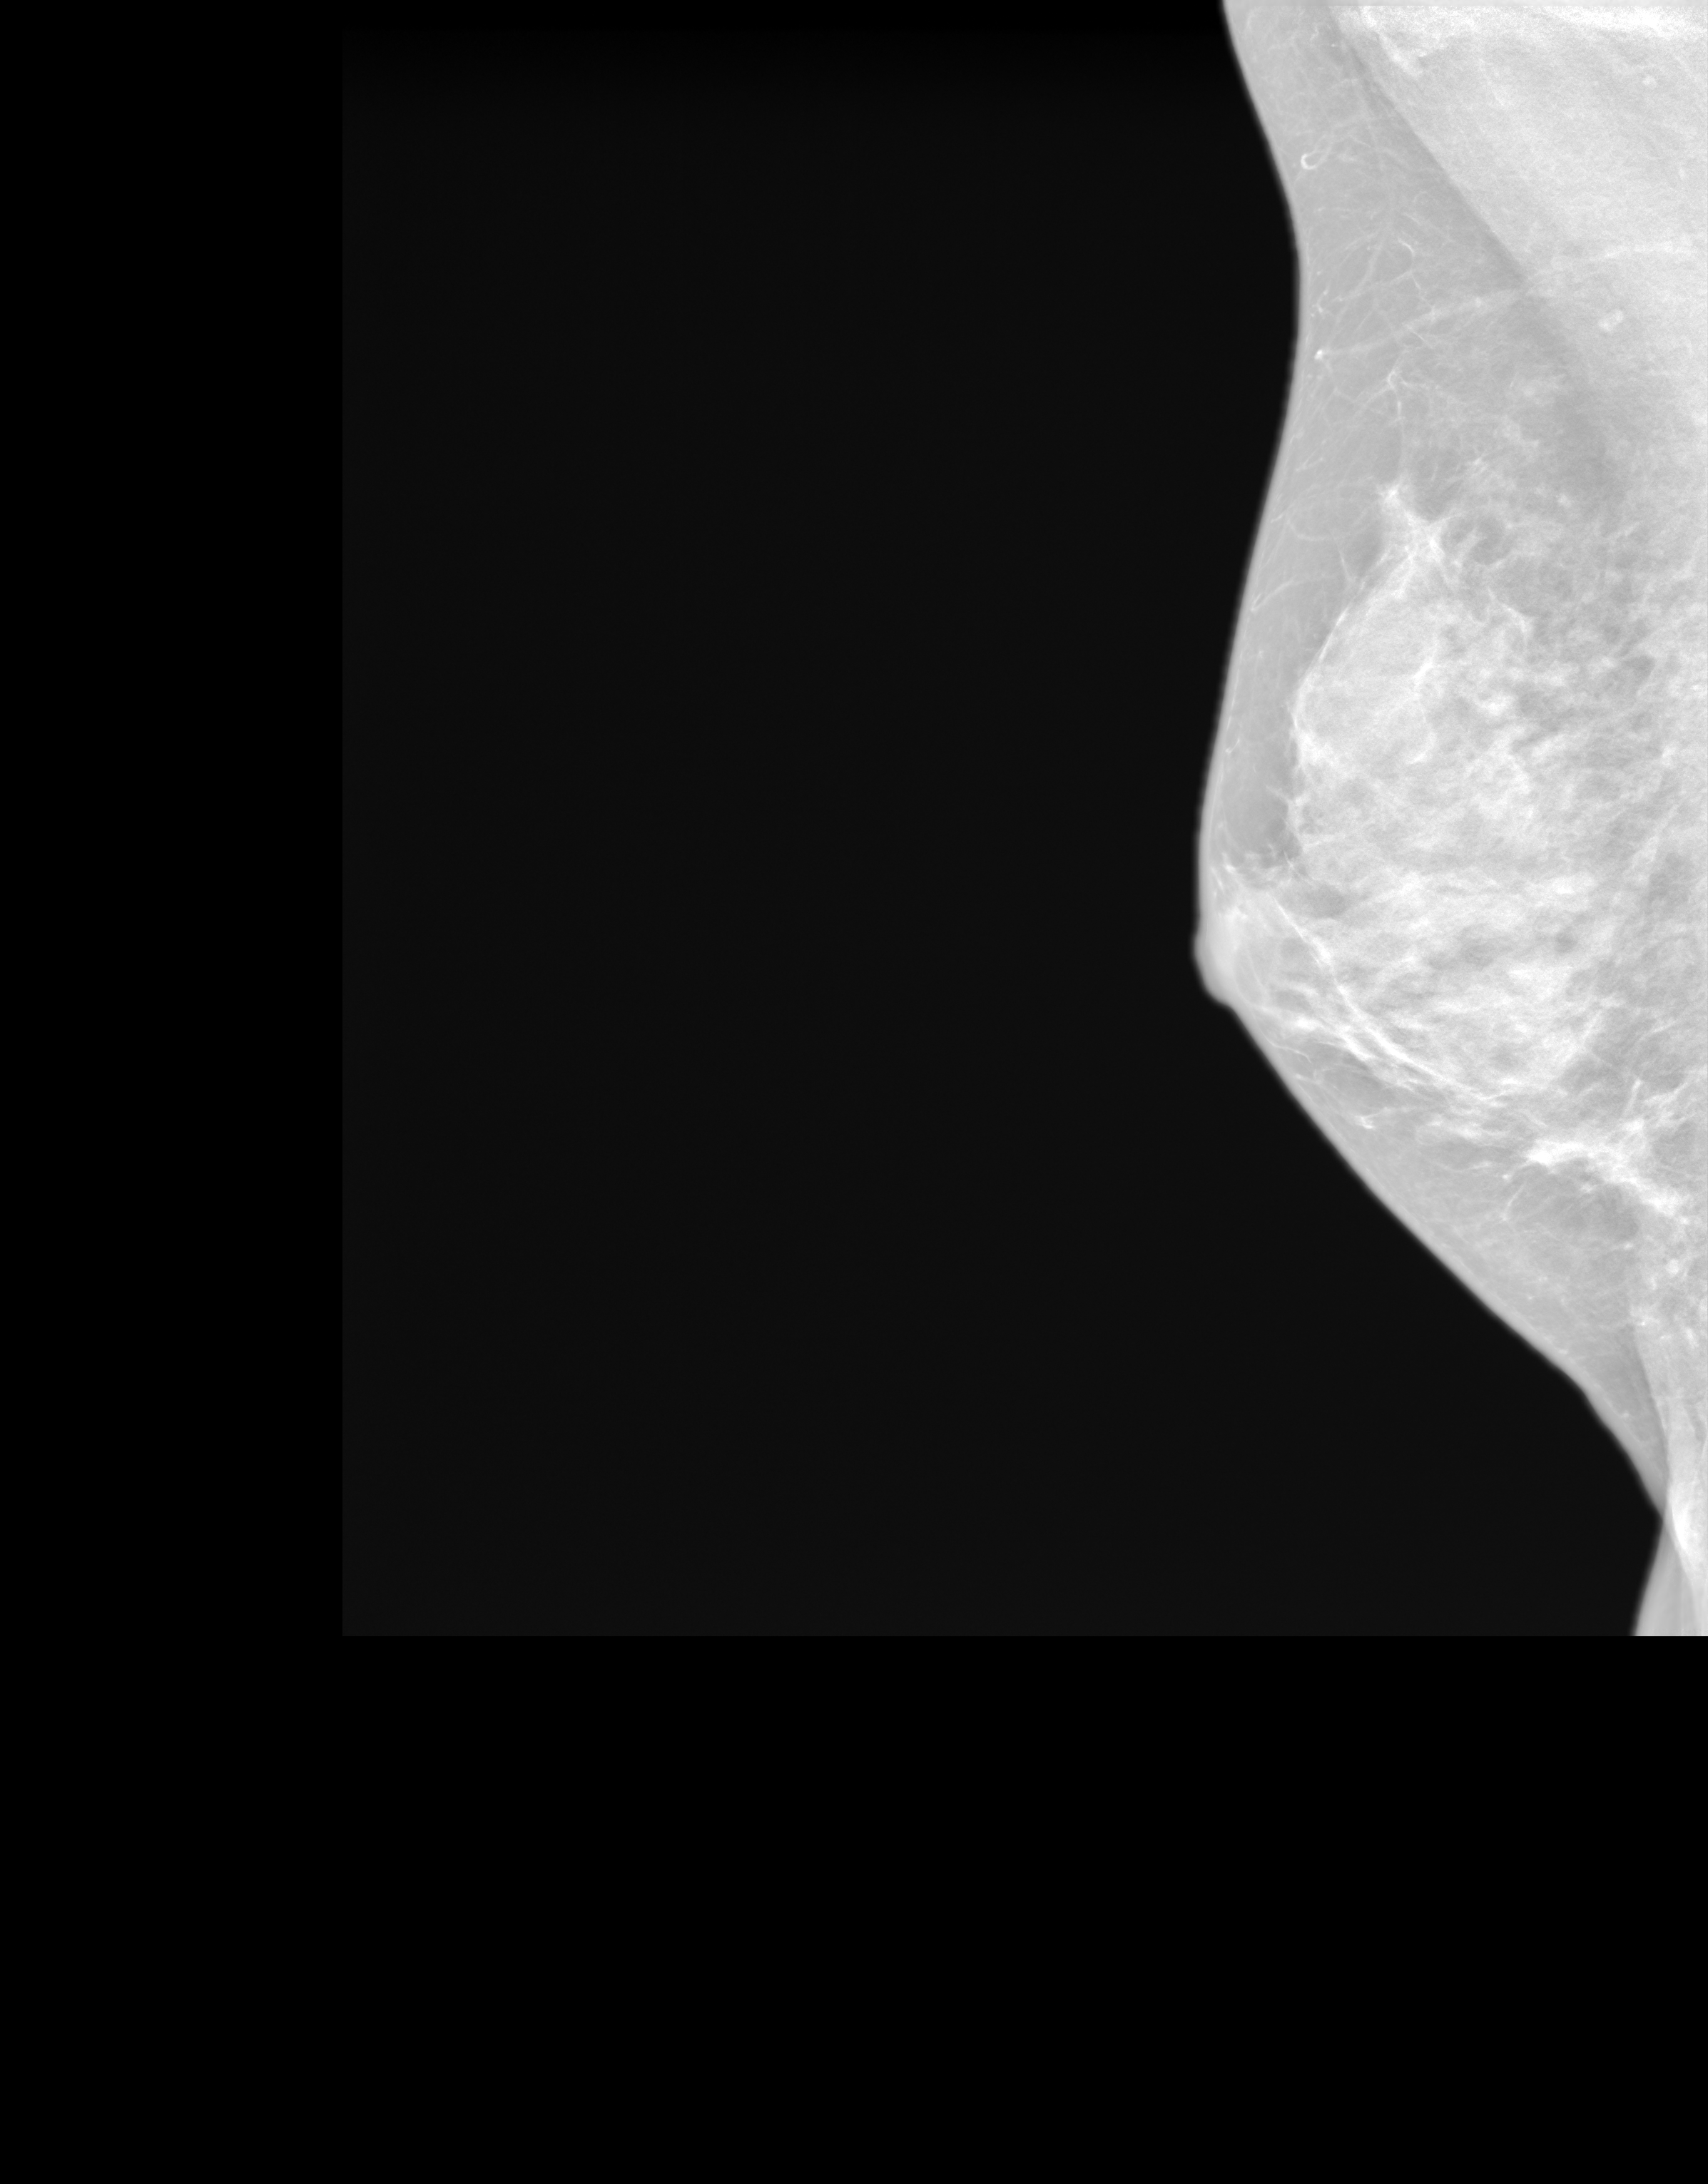
Screening examination, system: SenoIris_1SP2(440). Patient: female, 56 years.
Image type: synthesized 2-D view from tomosynthesis. Breast: right. Projection: medio-lateral oblique projection.